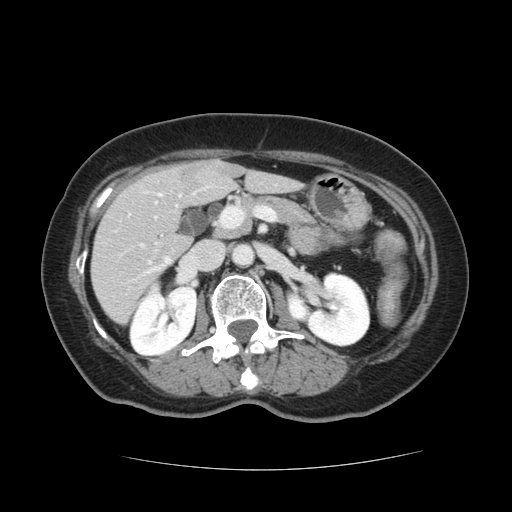
Contrast-enhanced abdominal CT, one axial slice; position 54 of 128 along the scan axis; 120 kVp; intravenous contrast given; soft-tissue window (W 400 / L 40 HU); 2.5 mm slice thickness; 512 × 512 image matrix, field of view 366 × 366 mm. Female patient, age 67 years. From the clinical record (not read from this slice): diagnosis: colorectal cancer liver metastases, imaged before liver resection; multiple liver metastases: yes; largest metastasis: 3 cm.
Structures marked on this image (manually delineated by an expert):
- hepatic veins: bounding box <130,256,172,287> (left, top, right, bottom; pixels)
- liver: <93,161,298,324>
- planned liver remnant (the part of the liver to remain after resection): <93,171,298,323>
- portal vein (with intrahepatic branches): <112,210,240,264>